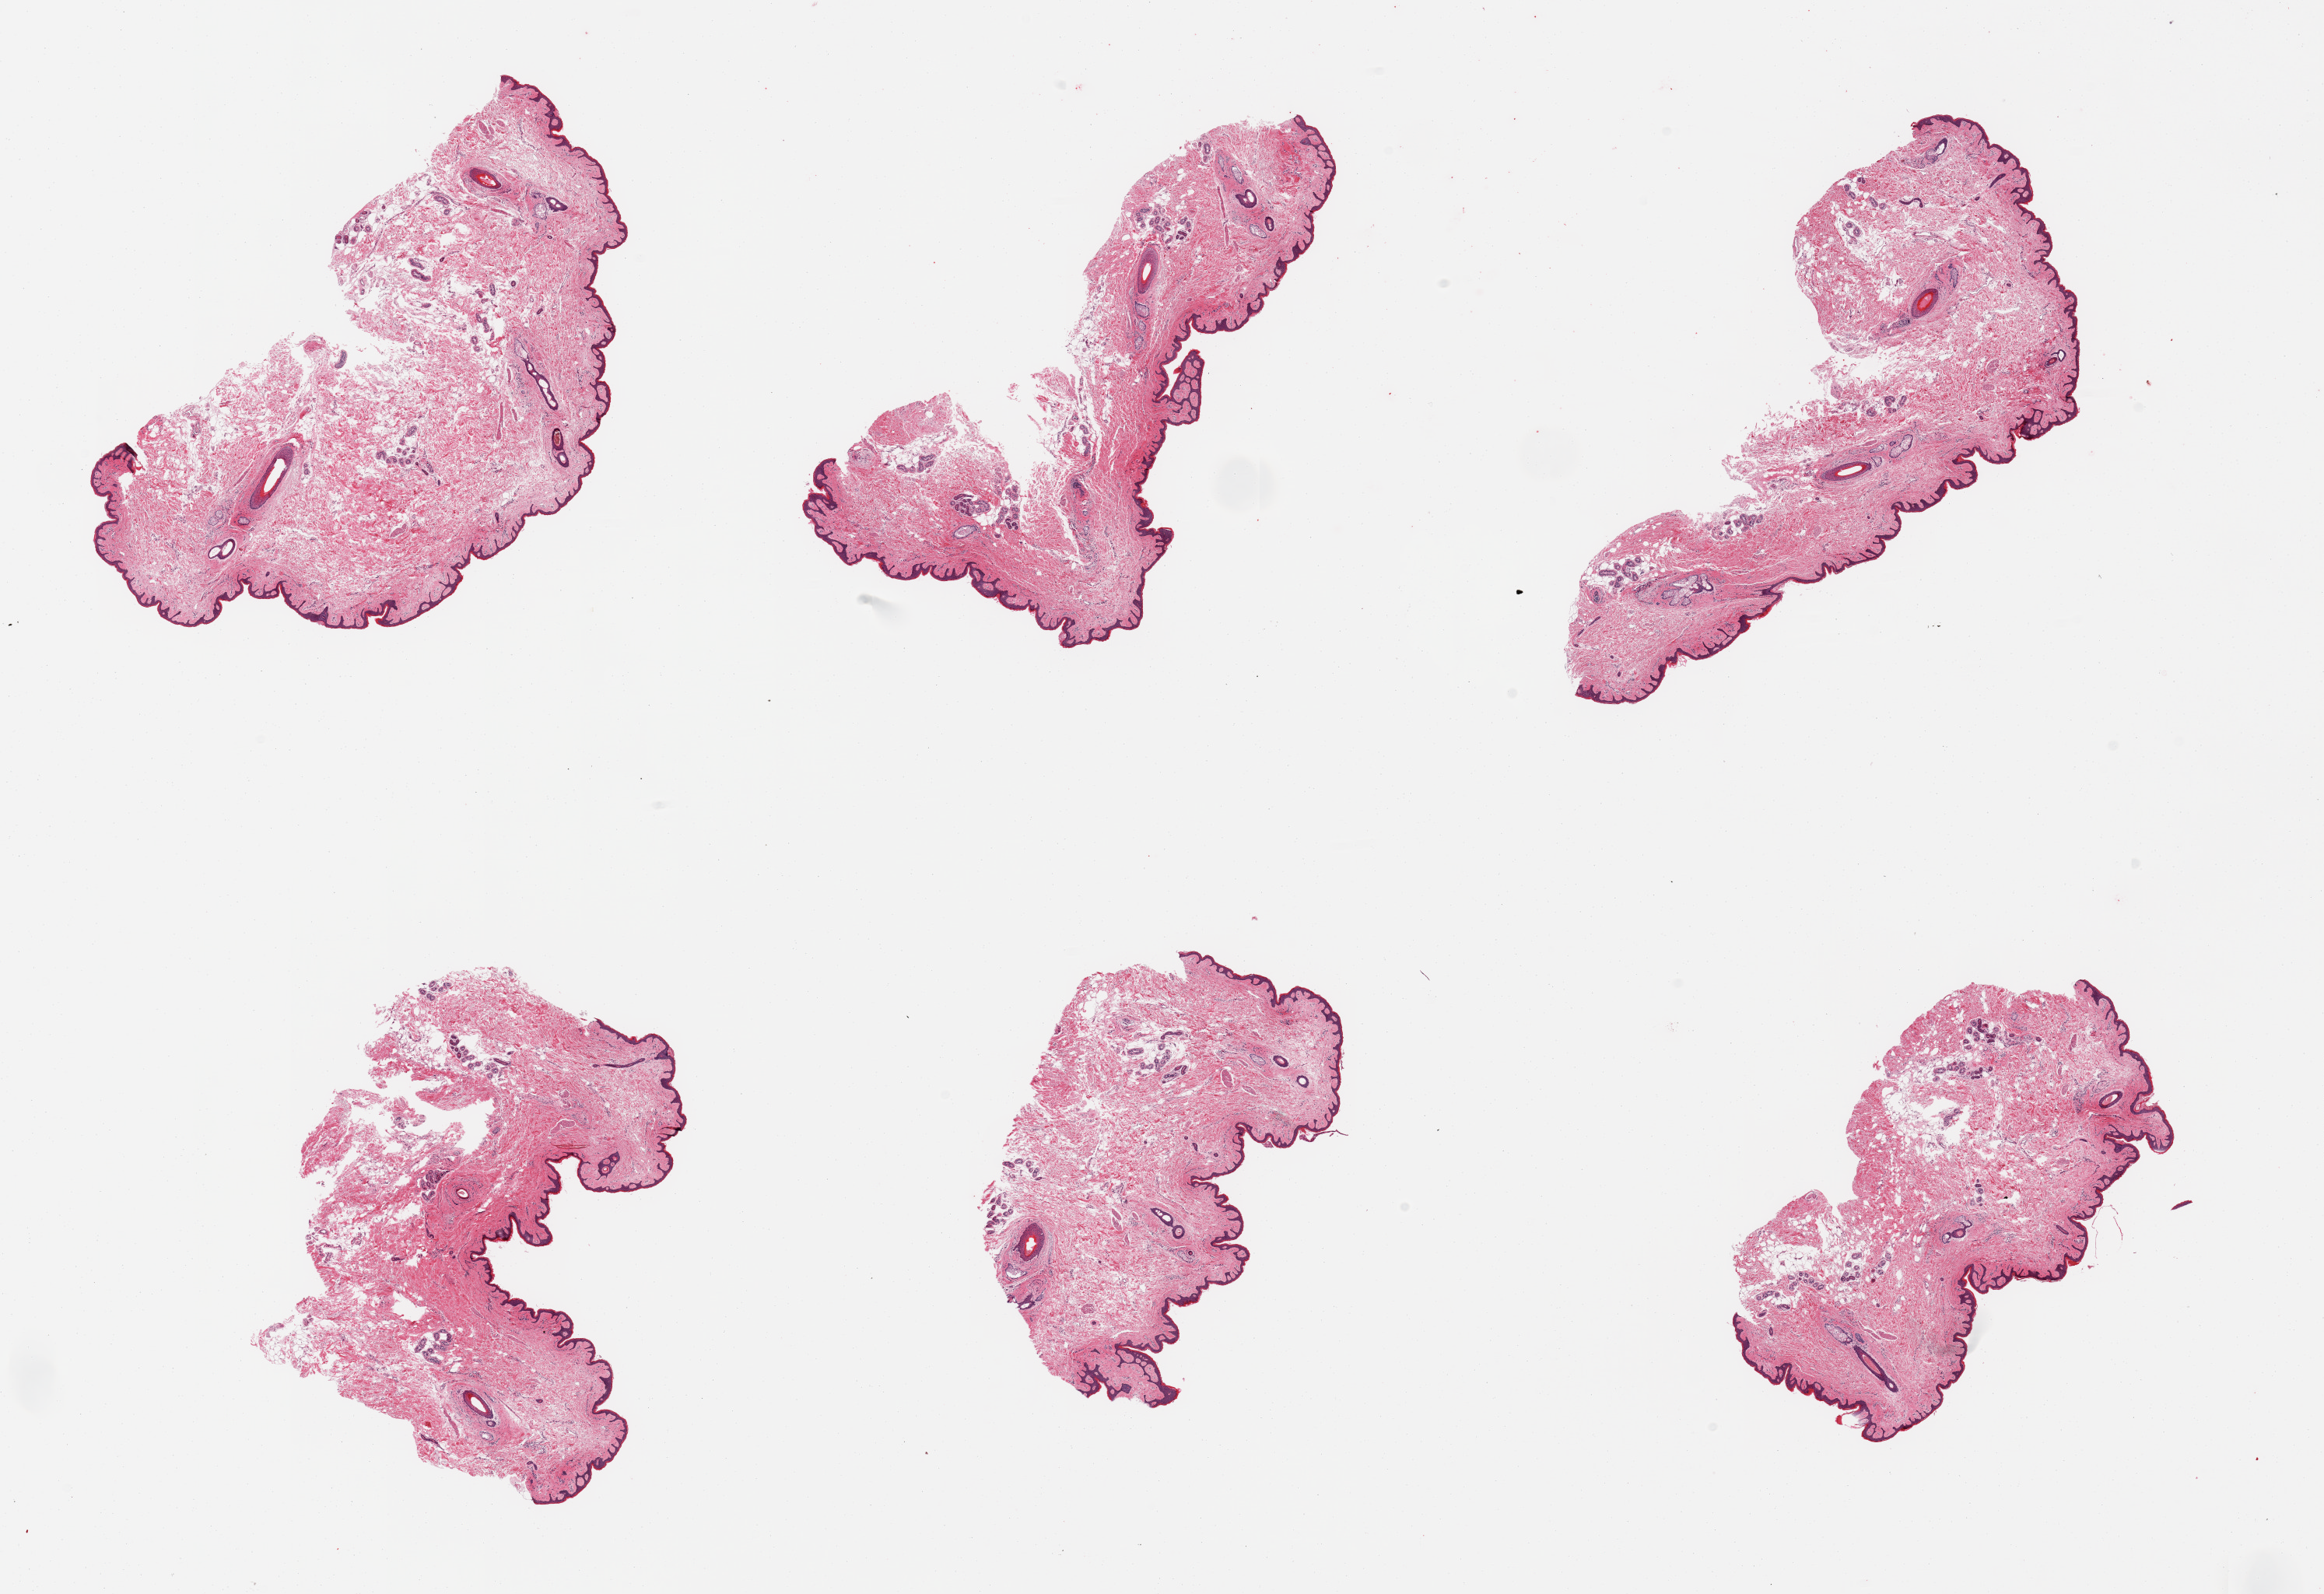
Whole-slide image, H&E stain — low-resolution overview of the scanned area, about 23.6 x 16.2 mm (acquisition: 20x scan); PAXgene-fixed paraffin-embedded (PFPE) section; target tissue: skin of suprapubic region; tissue donor sample. Donor sex: female.
Review note (as recorded): 6 pieces, squamous epithelium is ~30 microns, minimal adherent dermal fat.